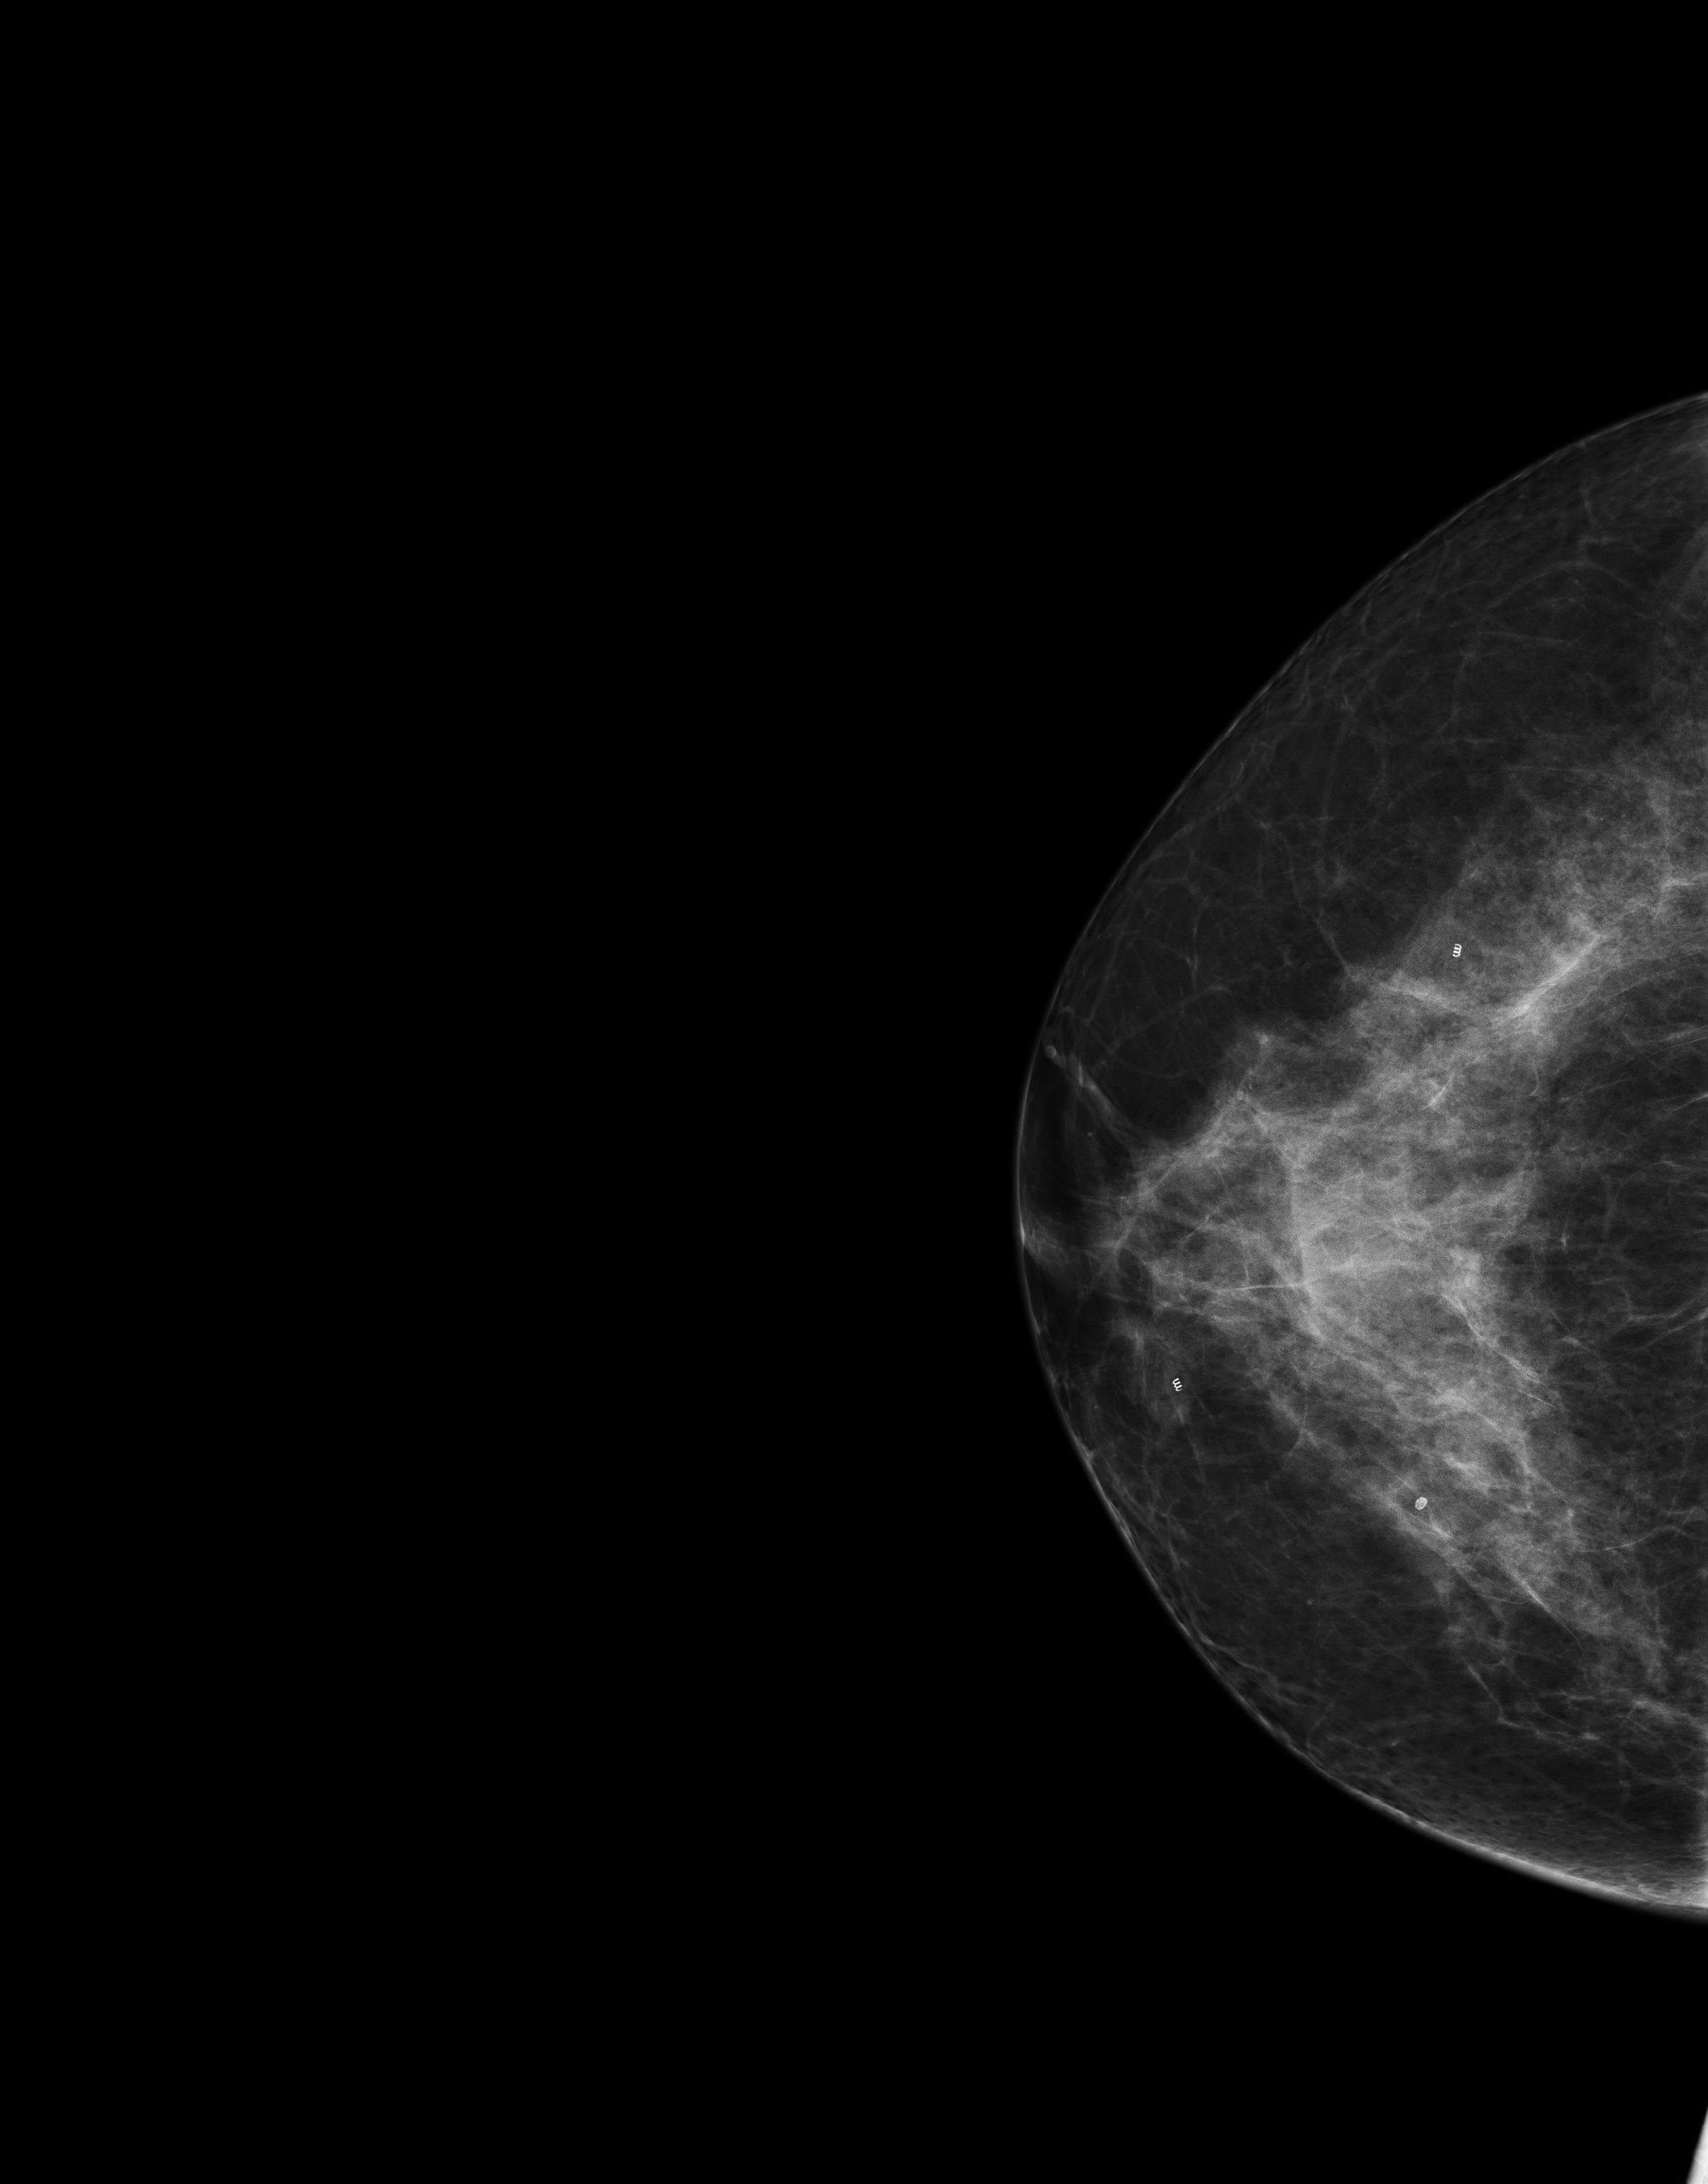
Screening examination, compressed breast thickness 68 mm, system: Senographe Essential ADS_56.21.3. Patient aged 47 years (female).
Image type: full-field digital mammogram. Breast: right. Projection: cranio-caudal projection.